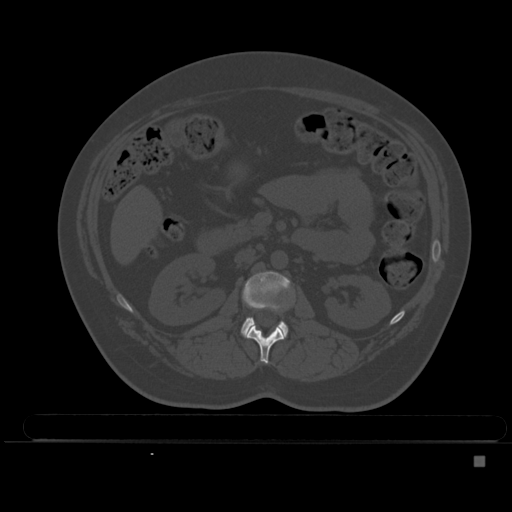
CT including the spine, one axial slice. Slice 184 of 495 in the series (ordered by position). Bone window (W 1800 / L 400 HU). 1.5 mm slice thickness. 512 × 512 image matrix. Female patient, age 33 years. From the clinical record (not read from this slice): primary cancer: breast.
Structures marked on this image (semi-automatic segmentation, software-assisted and operator-edited):
- L1 vertebra: bounding box [x1, y1, x2, y2] px = [245, 323, 284, 364]
- L2 vertebra: [241, 271, 290, 338]